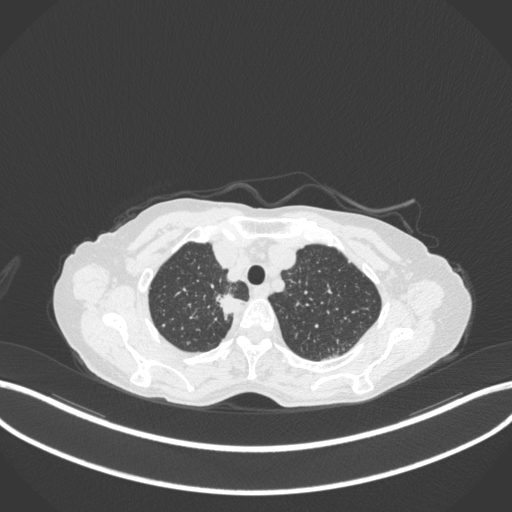
Chest CT, one axial slice. Slice 314 of 363 in the series (ordered by position). Reconstruction kernel B31f. 120 kVp. Lung window (W 1500 / L -600 HU). 1 mm slice thickness. 512 × 512 image matrix, field of view 400 × 400 mm. Female patient, age 75 years. Case-level facts recorded for this patient, not image findings: clinical TNM (as recorded): T1c N1 M1.
Outlined on this slice (bounding box drawn by a radiologist):
- lung tumour (recorded histology: adenocarcinoma): bounding box <212,287,249,318> (left, top, right, bottom; pixels)